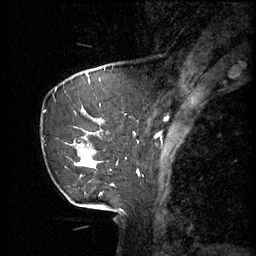
Breast MRI (dynamic contrast-enhanced), one sagittal slice. Slice 15 of 60 in the series (ordered by position). 3 images stored at this slice position (order not interpretable as contrast timing). 1.5 T. TE 4.2 ms, TR 11 ms. 2 mm slice thickness. 256 × 256 image matrix, field of view 220 × 220 mm. Patient: female, 69 years.
Outlined on this slice (semi-automatic segmentation, software-assisted and operator-edited):
- analysis volume of interest (the breast-tissue region the enhancement analysis was run in; not a lesion): box from (x=44, y=88) to (x=116, y=189) px
- tumour enhancement mask (voxels above the 70 % enhancement threshold inside the analysis volume of interest): (x=82, y=112)–(x=95, y=165)